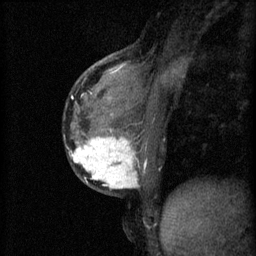
Breast MRI (dynamic contrast-enhanced), one sagittal slice; position 26 of 60 along the scan axis; 3 images stored at this slice position (order not interpretable as contrast timing); 1.5 T; TE 4.2 ms, TR 11 ms; 256 × 256 image matrix. Female patient, age 37 years.
Outlined on this slice (semi-automatically segmented with operator editing):
- analysis volume of interest (the breast-tissue region the enhancement analysis was run in; not a lesion): bounding box [x1, y1, x2, y2] px = [70, 118, 151, 195]
- tumour enhancement mask (voxels above the 70 % enhancement threshold inside the analysis volume of interest): [71, 130, 137, 189]